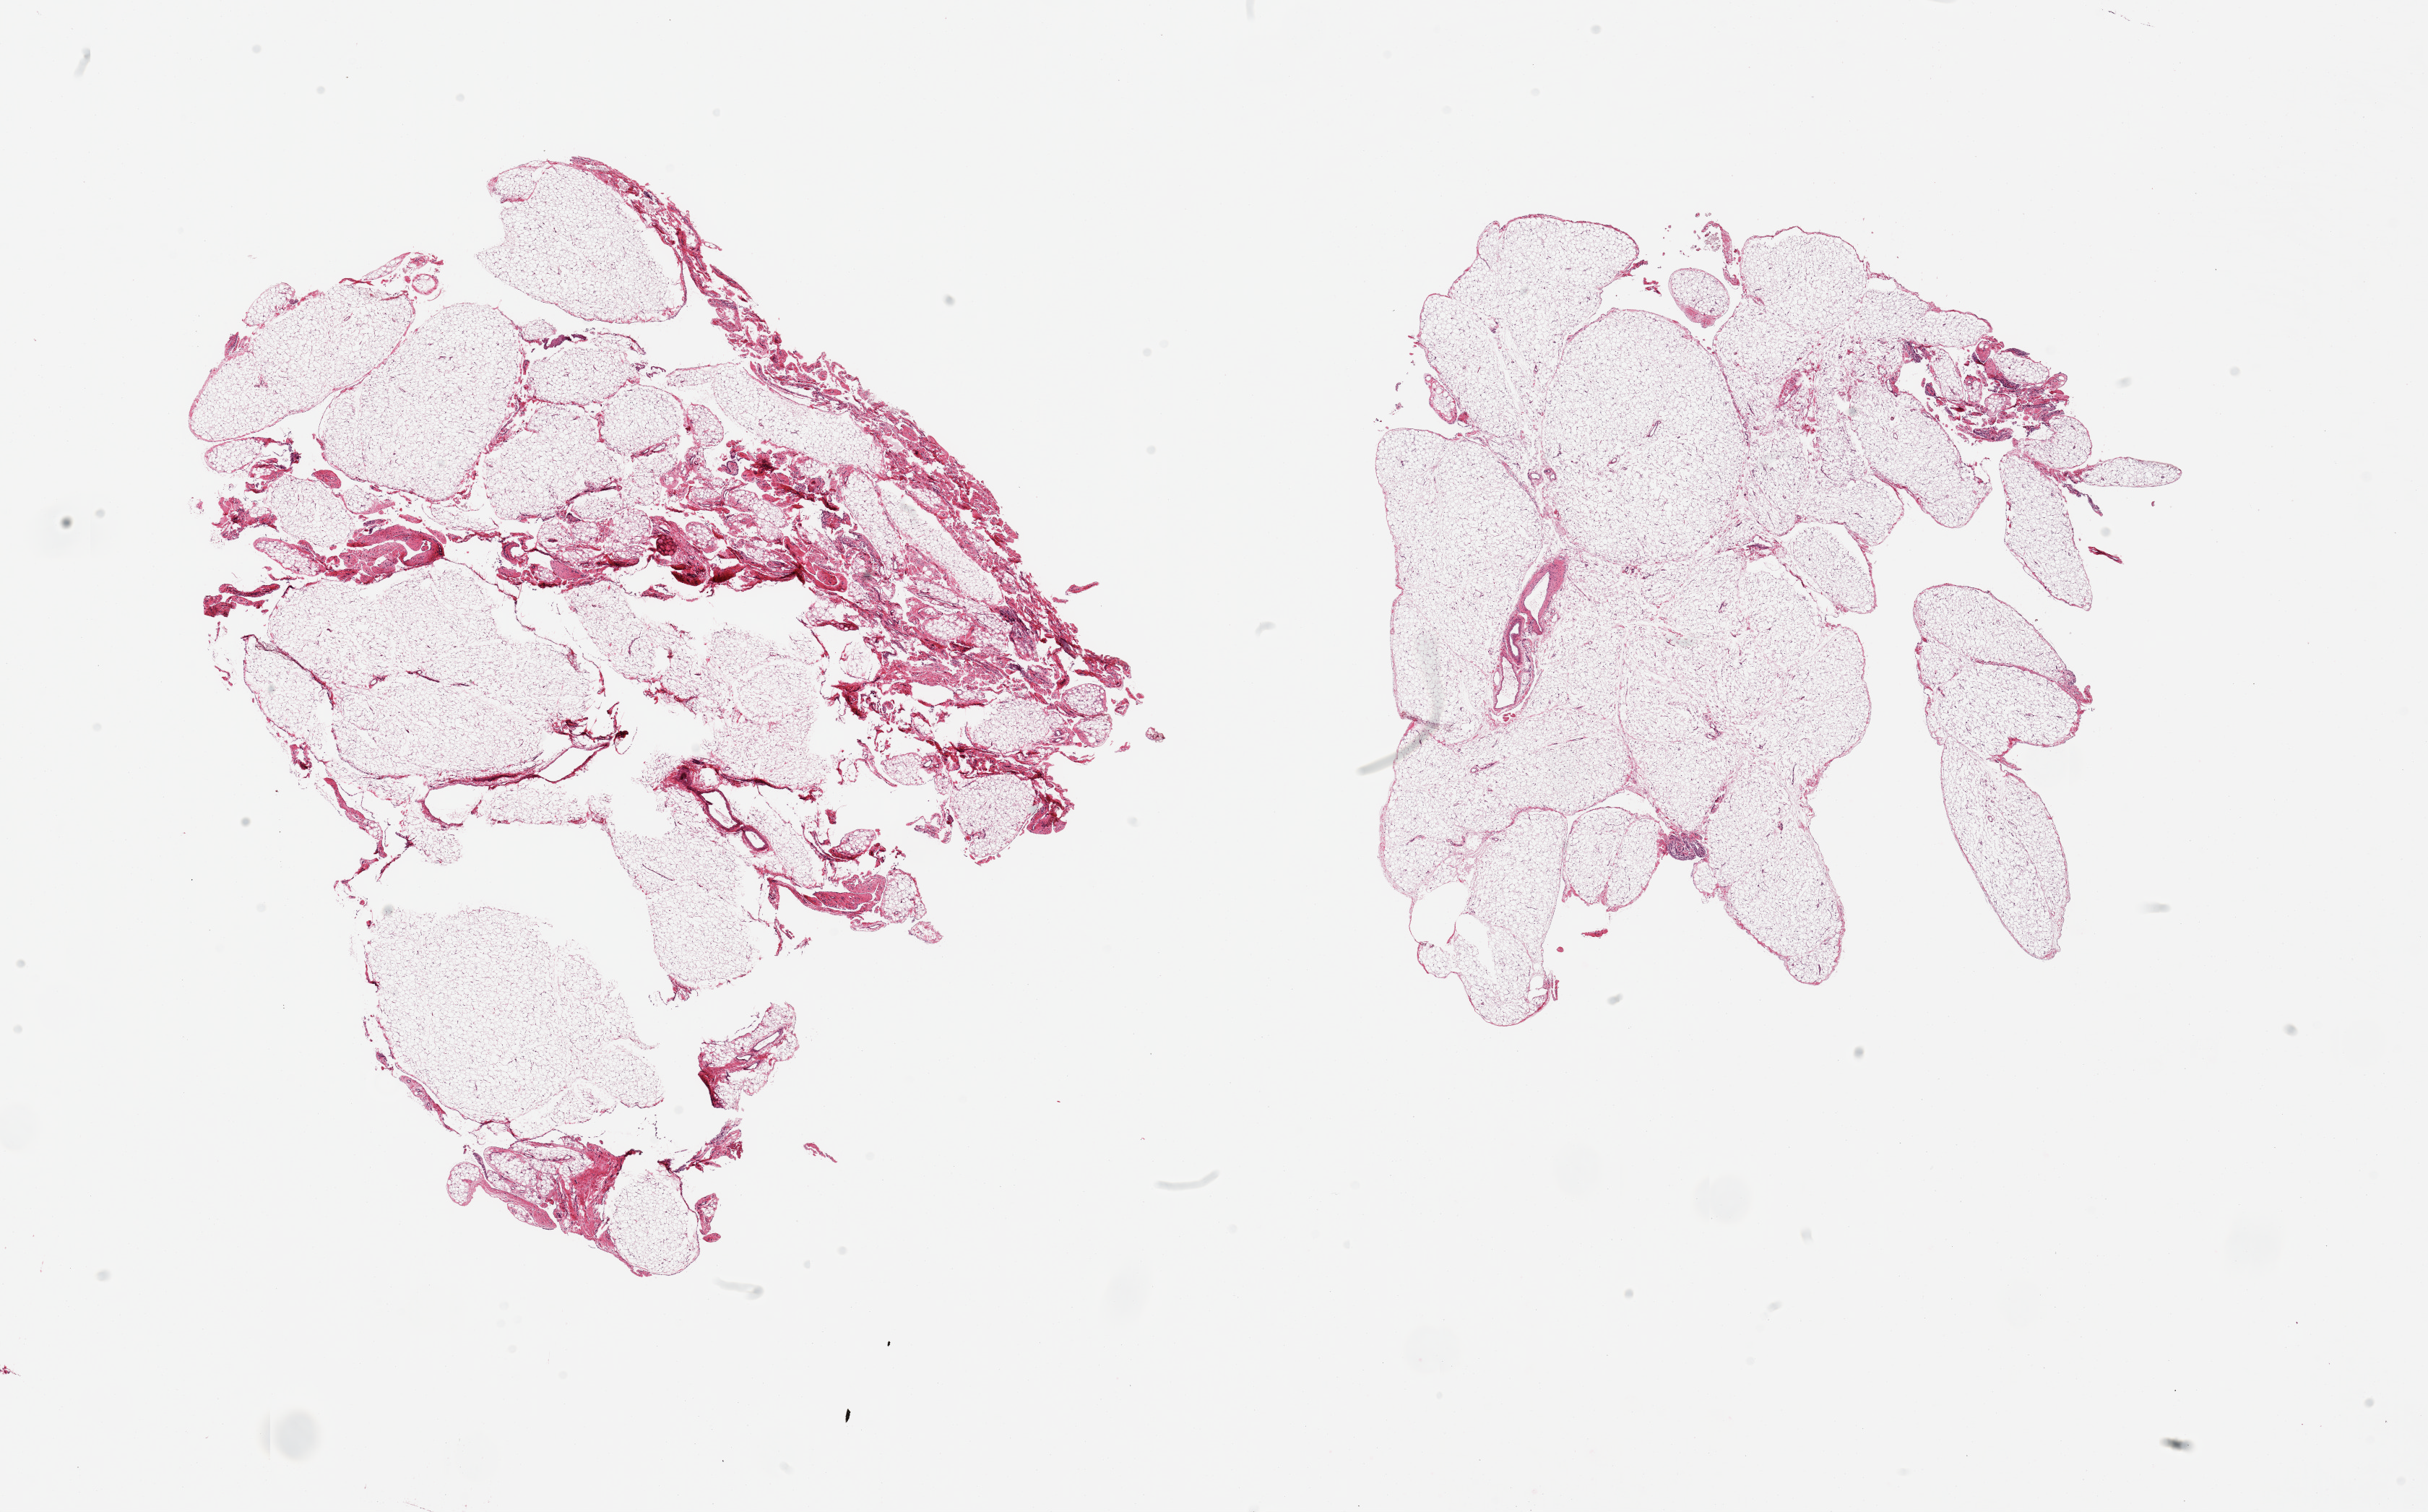
Whole-slide image, hematoxylin and eosin (H&E) stain — a low-resolution overview of the entire scanned area, about 26.6 x 16.6 mm (acquisition: 20x scan), PAXgene-fixed paraffin-embedded (PFPE) section, target tissue: omentum, tissue donor sample. Donor sex: female.
• review note (as recorded): 2 pieces